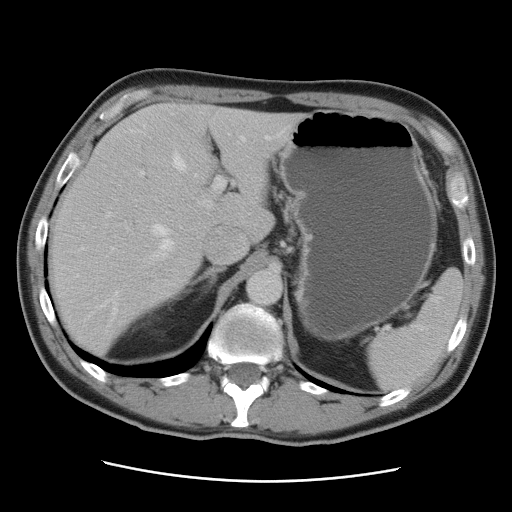
Contrast-enhanced abdominal CT, one axial slice. Position 61 of 89 along the scan axis. Intravenous contrast given. Soft-tissue window (W 400 / L 40 HU). 512 × 512 image matrix, field of view 366 × 366 mm. Male patient, age 59 years. From the clinical record (not read from this slice): diagnosis: colorectal cancer liver metastases, imaged before liver resection; multiple liver metastases: yes; largest metastasis: 0.6 cm; disease in both lobes: yes.
Outlined on this slice (outlined manually by an expert reader):
- hepatic veins: box from (x=81, y=136) to (x=270, y=305) px
- liver: (x=49, y=103)–(x=306, y=355)
- planned liver remnant (the part of the liver to remain after resection): (x=88, y=104)–(x=275, y=243)
- portal vein (with intrahepatic branches): (x=128, y=171)–(x=226, y=230)